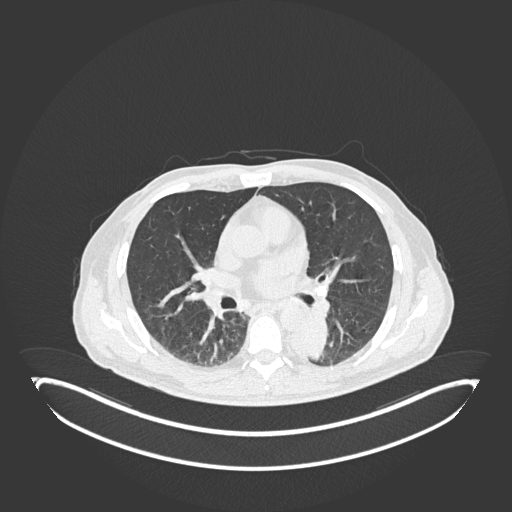
Chest CT, one axial slice. Position 106 of 251 along the scan axis. 120 kVp. Lung window (W 1500 / L -600 HU). 1 mm slice thickness. 512 × 512 image matrix, field of view 500 × 500 mm. Male patient, age 72 years. Case-level facts recorded for this patient, not image findings: clinical TNM (as recorded): T2b N0 M1.
Structures marked on this image (rectangle marked by the reading radiologist):
- lung tumour (recorded histology: adenocarcinoma): bounding box [x1, y1, x2, y2] px = [291, 320, 333, 360]